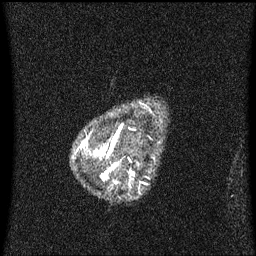
Breast MRI (dynamic contrast-enhanced), one sagittal slice. Slice 51 of 60 in the series (ordered by position). Dynamic contrast-enhanced series, image 2 of 3 at this slice position (ordered by acquisition). 1.5 T. TE 4.2 ms, TR 8.4 ms. 2 mm slice thickness. 256 × 256 image matrix, field of view 200 × 200 mm. Female patient, age 48 years. From the clinical record (not read from this slice): setting: breast cancer imaged before/during neoadjuvant chemotherapy; receptor status: HR-positive, HER2-negative.
Annotated regions visible in this slice (semi-automatic segmentation, software-assisted and operator-edited):
- analysis volume of interest (the breast-tissue region the enhancement analysis was run in; not a lesion): bounding box (x1, y1, x2, y2) in pixels: (80, 134, 133, 186)
- tumour enhancement mask (voxels above the 70 % enhancement threshold inside the analysis volume of interest): (112, 137, 133, 175)